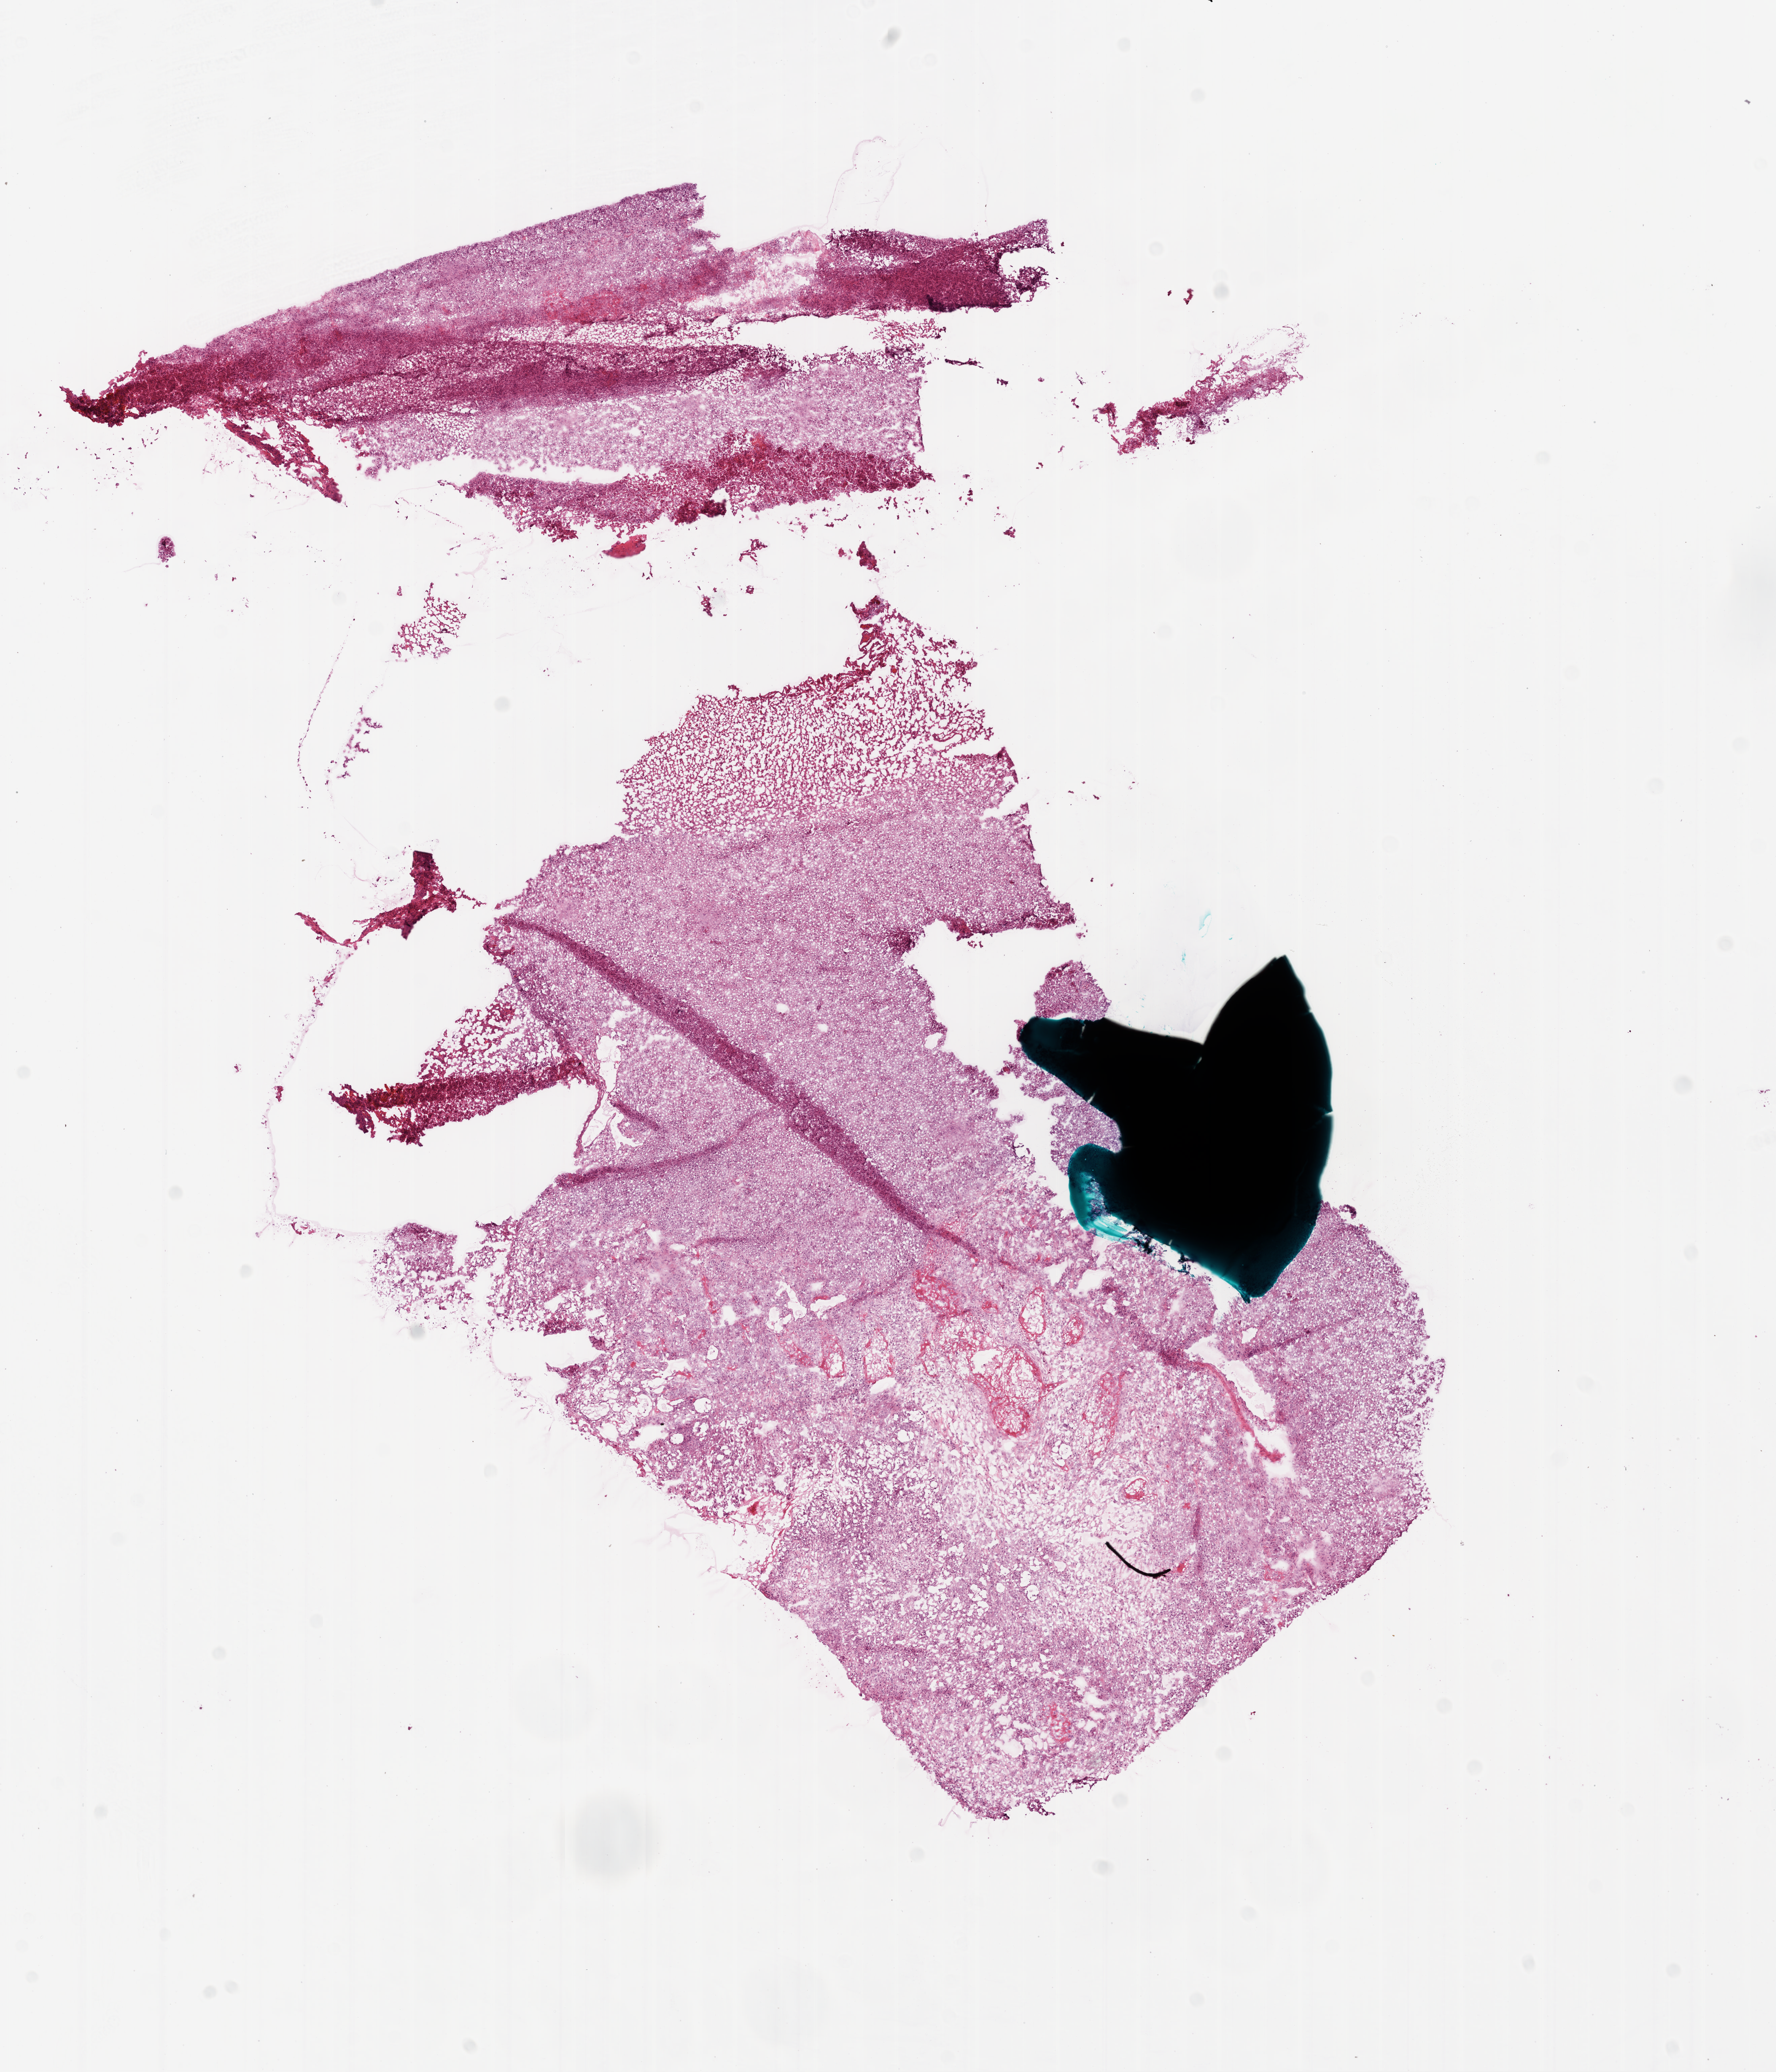
Digitized Hematoxylin and eosin (H&E) stained tissue section (whole slide), whole scanned area (about 10.6 x 12.4 mm, from a 20x scan) shown as a low-resolution overview, frozen section from the bottom of the tissue portion, sample: primary tumour, brain. Patient: female, age at initial diagnosis 48 years. Composition of this section per pathologist review: tumour cells 100%, tumour nuclei 100%, normal cells 0%, stromal cells 0%, necrosis 0%.
* pathologic diagnosis: Glioblastoma